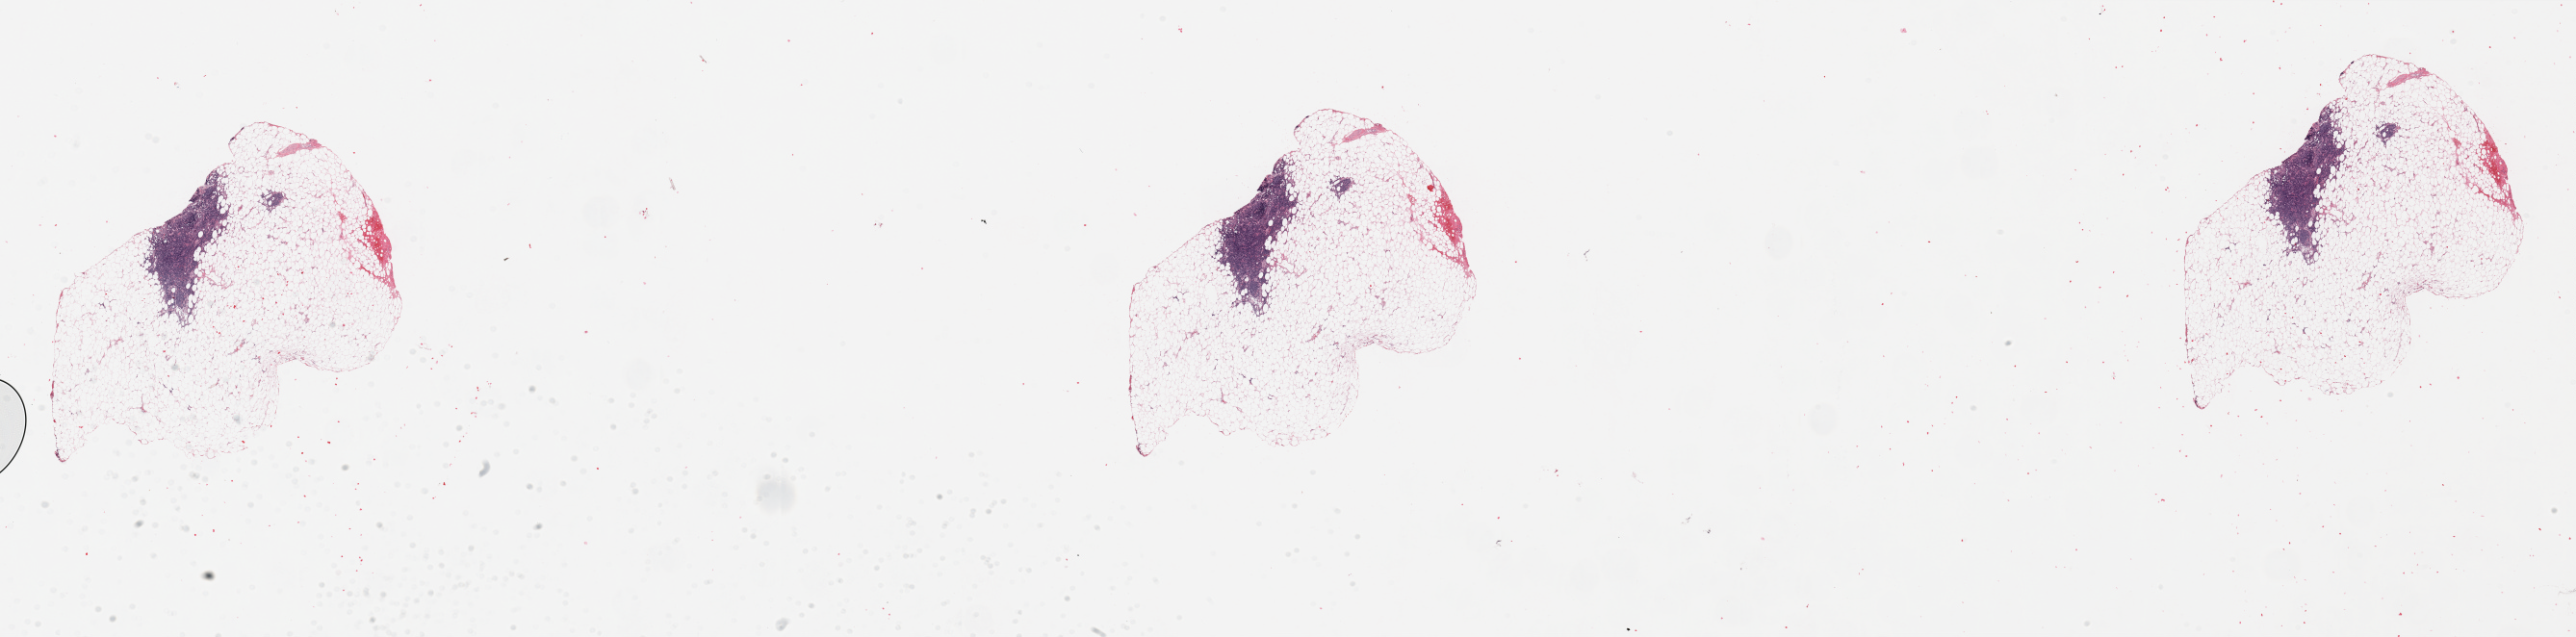
Whole-slide histology image, H&E-stained — whole scanned area (about 42.3 x 10.5 mm, slide scanned at 20x) shown as a low-resolution overview, pancreas, normal (non-tumour) tissue. Male, 55 y/o.
* this section: normal (non-tumour) tissue from the same patient
* patient diagnosis: Infiltrating duct carcinoma, NOS